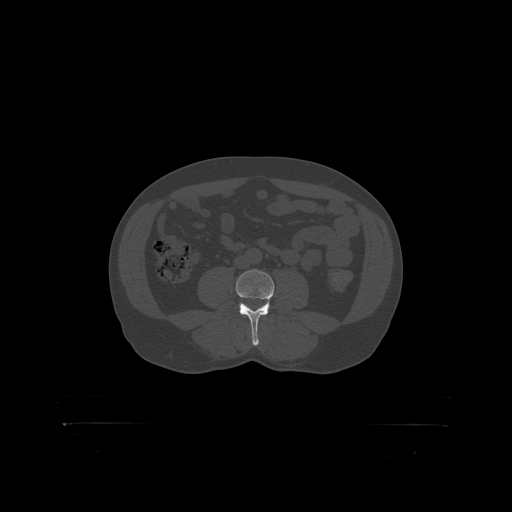
CT including the spine, one axial slice; position 234 of 399 along the scan axis; reconstruction kernel STANDARD; bone window (W 1800 / L 400 HU); 1.25 mm slice thickness; 512 × 512 image matrix. Patient: male, 46 years. From the clinical record (not read from this slice): primary cancer: skin.
Structures marked on this image (semi-automatically segmented with operator editing):
- L4 vertebra: box from (x=236, y=270) to (x=275, y=319) px